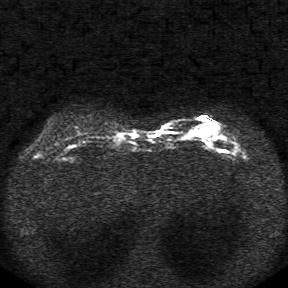
Breast MRI, one axial slice; slice 8 of 34 in the series (ordered by position); diffusion-weighted series; image 2 of 4 stored at this slice position (different b-values; order by instance number); 1.5 T; 5 mm slice thickness; 288 × 288 image matrix. Female patient.
Annotated regions visible in this slice (outlined manually by an expert reader):
- tumour on diffusion-weighted imaging: box from (x=196, y=117) to (x=217, y=138) px